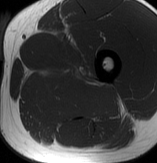
MRI of an extremity soft-tissue mass, one axial slice; slice 49 of 70 in the series (ordered by position); MR volume resampled by the dataset authors to the PET/CT grid (not the native acquisition matrix); 157 × 163 image matrix, field of view 153 × 159 mm. Male patient. From the clinical record (not read from this slice): histological type: extraskeletal osteosarcoma; grade: high; site of the primary tumour: left adductur.
Structures marked on this image (expert contour drawn on MRI and transferred to this co-registered scan by the dataset authors):
- gross tumour volume (mass): bounding box (x1, y1, x2, y2) in pixels: (33, 62, 121, 121)